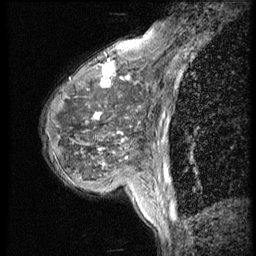
Breast MRI (dynamic contrast-enhanced), one sagittal slice. Slice 16 of 56 in the series (ordered by position). 4 images stored at this slice position (order not interpretable as contrast timing). 1.5 T. TE 4.2 ms, TR 9 ms. 2.5 mm slice thickness. 256 × 256 image matrix, field of view 180 × 180 mm. Female patient, age 50 years. Case-level facts recorded for this patient, not image findings: setting: breast cancer imaged before/during neoadjuvant chemotherapy; receptor status: triple-negative.
Outlined on this slice (semi-automatic segmentation, software-assisted and operator-edited):
- analysis volume of interest (the breast-tissue region the enhancement analysis was run in; not a lesion): bounding box <39,46,148,188> (left, top, right, bottom; pixels)
- tumour enhancement mask (voxels above the 140 % enhancement threshold inside the analysis volume of interest): <97,71,125,118>